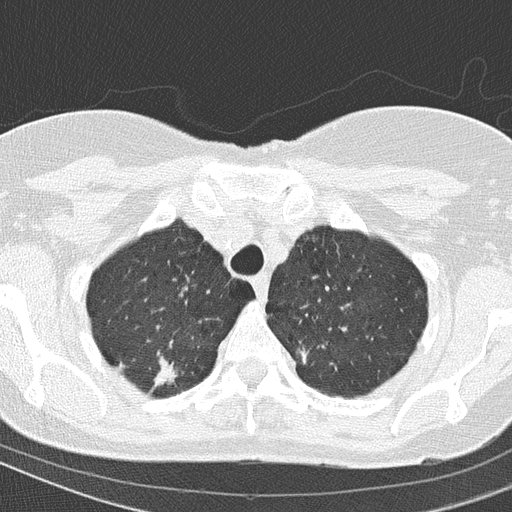
Low-dose screening chest CT, one axial slice. Position 130 of 154 along the scan axis. Reconstruction kernel B50f. 120 kVp. Lung window (W 1500 / L -600 HU). 2 mm slice thickness. 512 × 512 image matrix, field of view 288 × 288 mm.
Outlined on this slice (outlined manually by an expert reader):
- lesion 1 (tumor, upper lobe of right lung): bounding box [x1, y1, x2, y2] px = [154, 356, 178, 387]